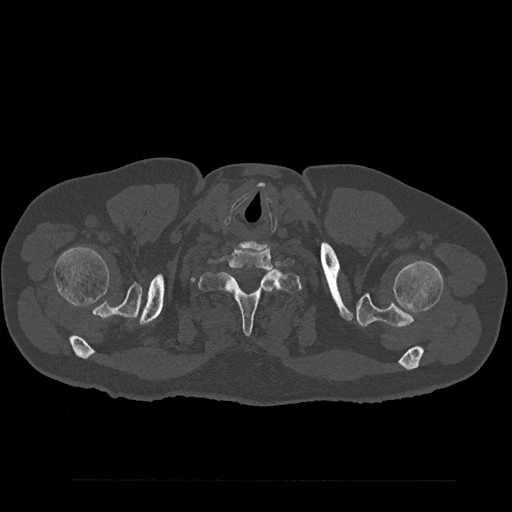
CT including the spine, one axial slice. Slice 763 of 797 in the series (ordered by position). Bone window (W 1800 / L 400 HU). 0.5 mm slice thickness. 512 × 512 image matrix, field of view 430 × 430 mm. Male patient, age 61 years. Case-level facts recorded for this patient, not image findings: primary cancer: prostate.
Structures marked on this image (semi-automatically segmented with operator editing):
- T1 vertebra: bounding box (x1, y1, x2, y2) in pixels: (198, 261, 301, 335)